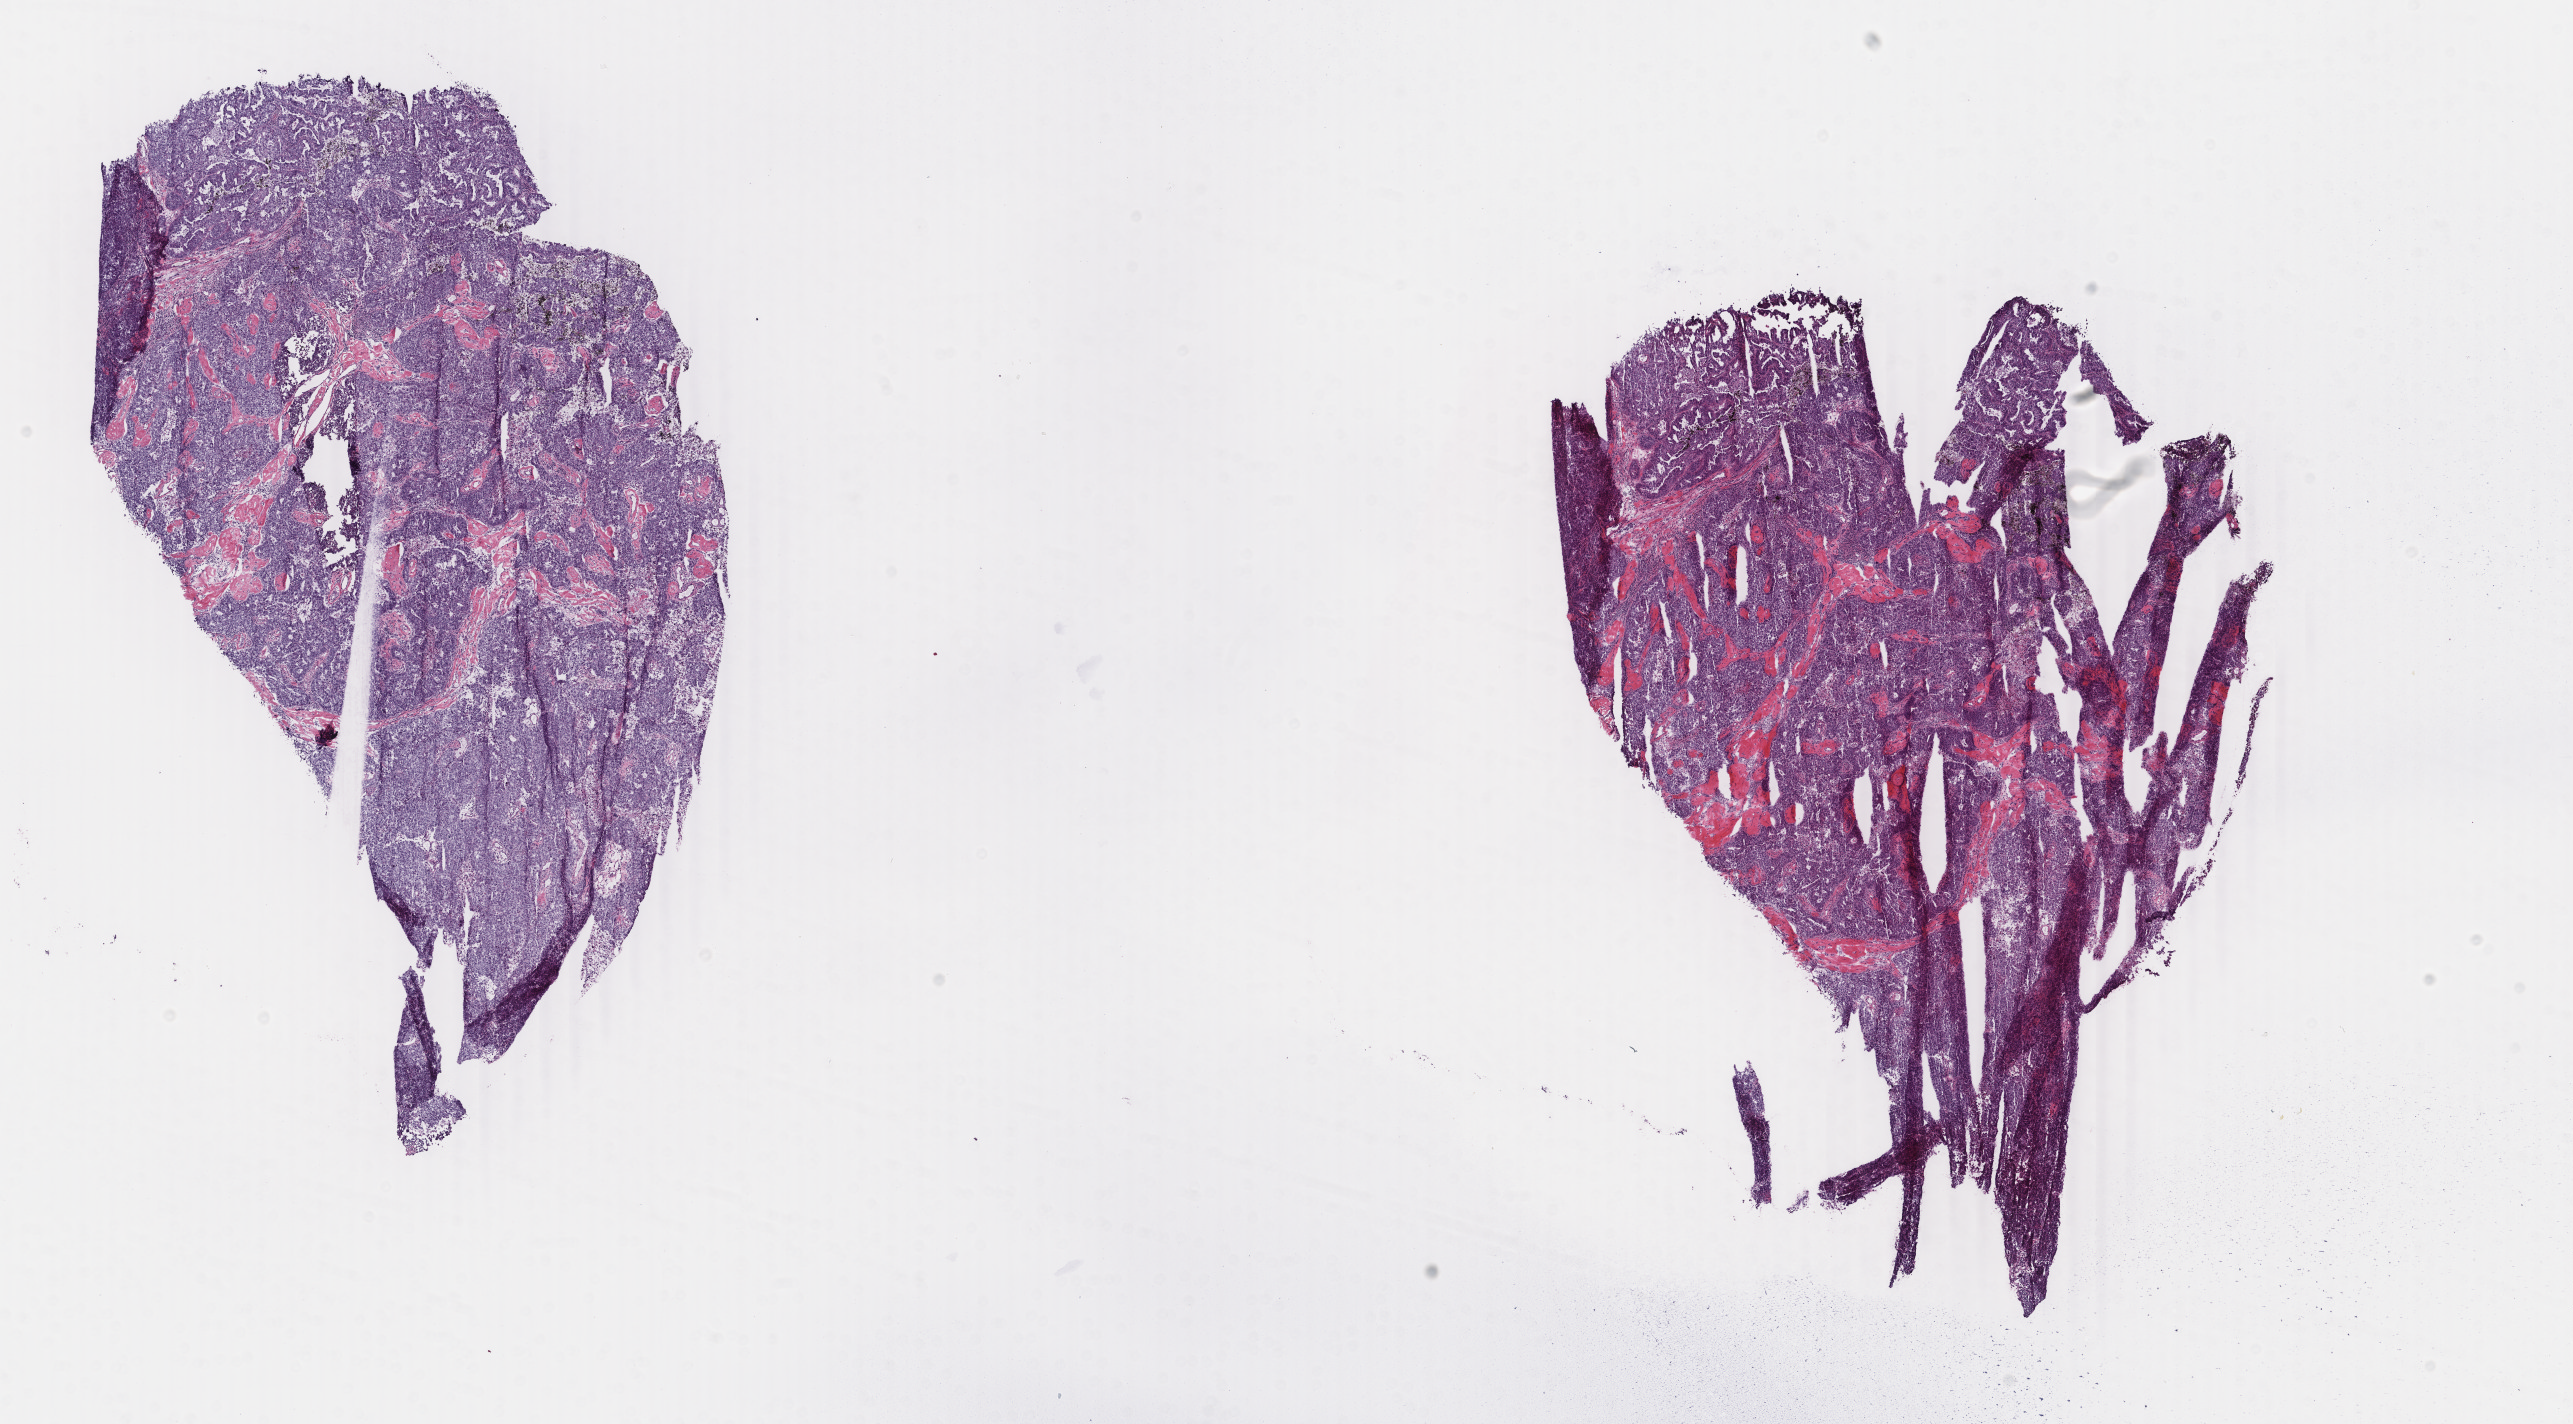
Whole-slide histology image, Hematoxylin and eosin (H&E) stained, whole scanned area (about 20.5 x 11.3 mm, slide scanned at 40x) shown as a low-resolution overview; frozen section from the top of the tissue portion; primary tumour sample from the uterus. Patient: female, age at initial diagnosis 74 years. Histologic grade: G3 (poorly differentiated). Pathologist review of this section (percent, as recorded): tumour cells 60%, tumour nuclei 80%, normal cells 0%, stromal cells 20%, necrosis 20%. Infiltration values recorded for this section: lymphocyte infiltration 20%, monocyte infiltration 10%, neutrophil infiltration 20%.
• lymph nodes positive (case pathology): 0 of 24 examined
• histologic diagnosis: Endometrioid adenocarcinoma, NOS (endometrium)
• FIGO stage: IB